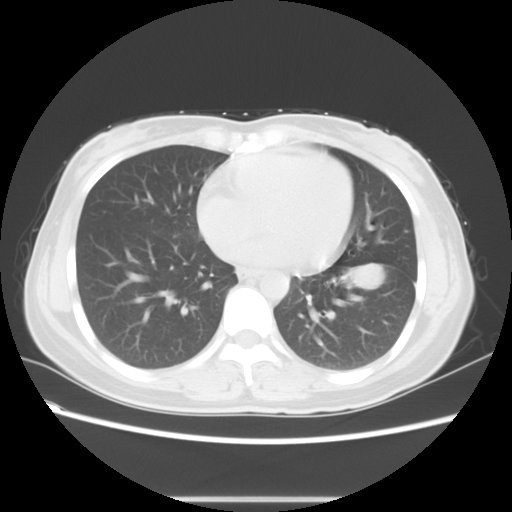
Chest CT, one axial slice; slice 24 of 56 in the series (ordered by position); reconstruction kernel STANDARD; lung window (W 1500 / L -600 HU); 5 mm slice thickness; 512 × 512 image matrix, field of view 350 × 350 mm. Patient: female, 41 years. From the clinical record (not read from this slice): clinical TNM (as recorded): T1c N3 M1b.
Structures marked on this image (rectangle marked by the reading radiologist):
- lung tumour (recorded histology: adenocarcinoma): bounding box <343,259,389,301> (left, top, right, bottom; pixels)